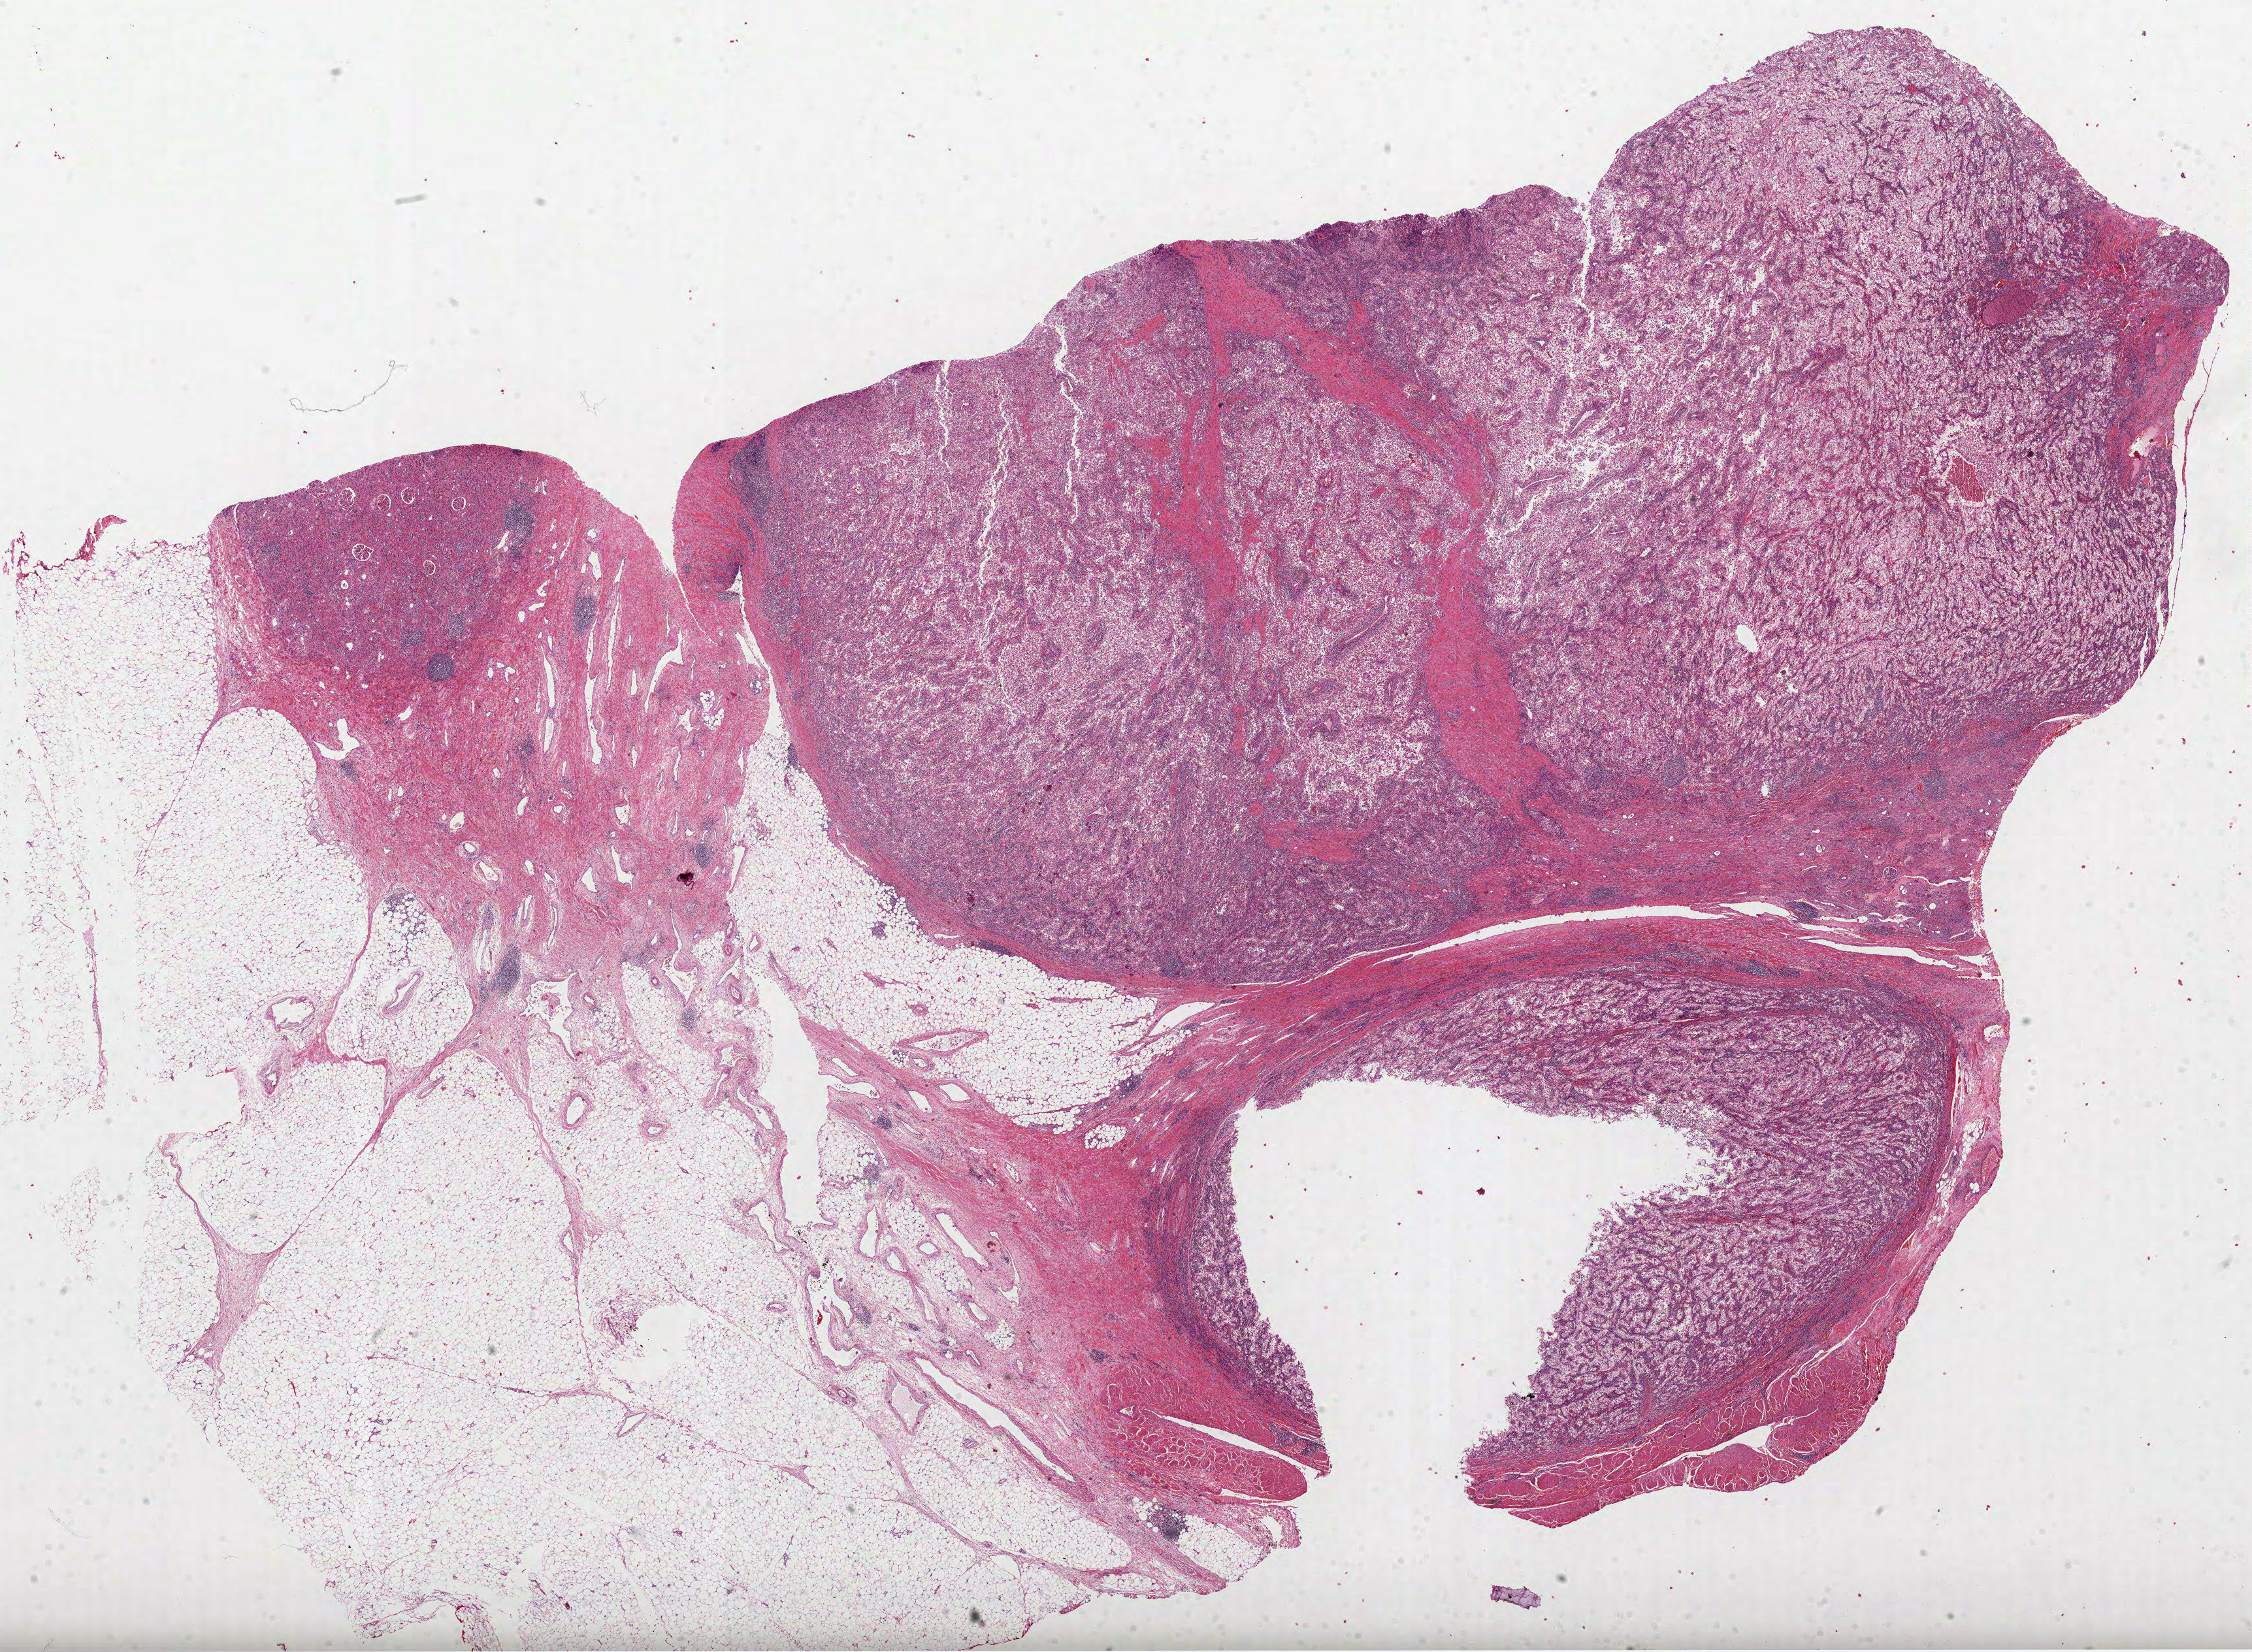
Digitized H&E tissue section (whole slide), shown as a low-resolution overview of the whole scanned area (about 27.8 x 20.4 mm), formalin-fixed paraffin-embedded (FFPE) diagnostic section, primary tumour sample from the kidney. Patient: female, age at initial diagnosis 46 years. Histologic grade: G4 (undifferentiated).
Laterality: right. AJCC pathologic stage: IV. Diagnosis: Clear cell adenocarcinoma, NOS.